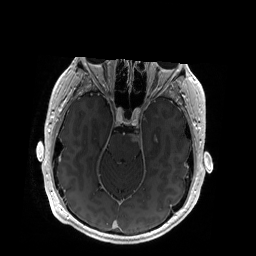
Brain MRI from a brain-tumour surgery series, one axial slice; position 123 of 192 along the scan axis; T1-weighted post-contrast; 1 mm slice thickness; 256 × 256 image matrix. Case-level facts recorded for this patient, not image findings: histopathology: Glioblastoma; WHO grade: 4; IDH mutation: no.
Structures marked on this image (expert manual segmentation):
- tumour: box from (x=132, y=134) to (x=157, y=145) px